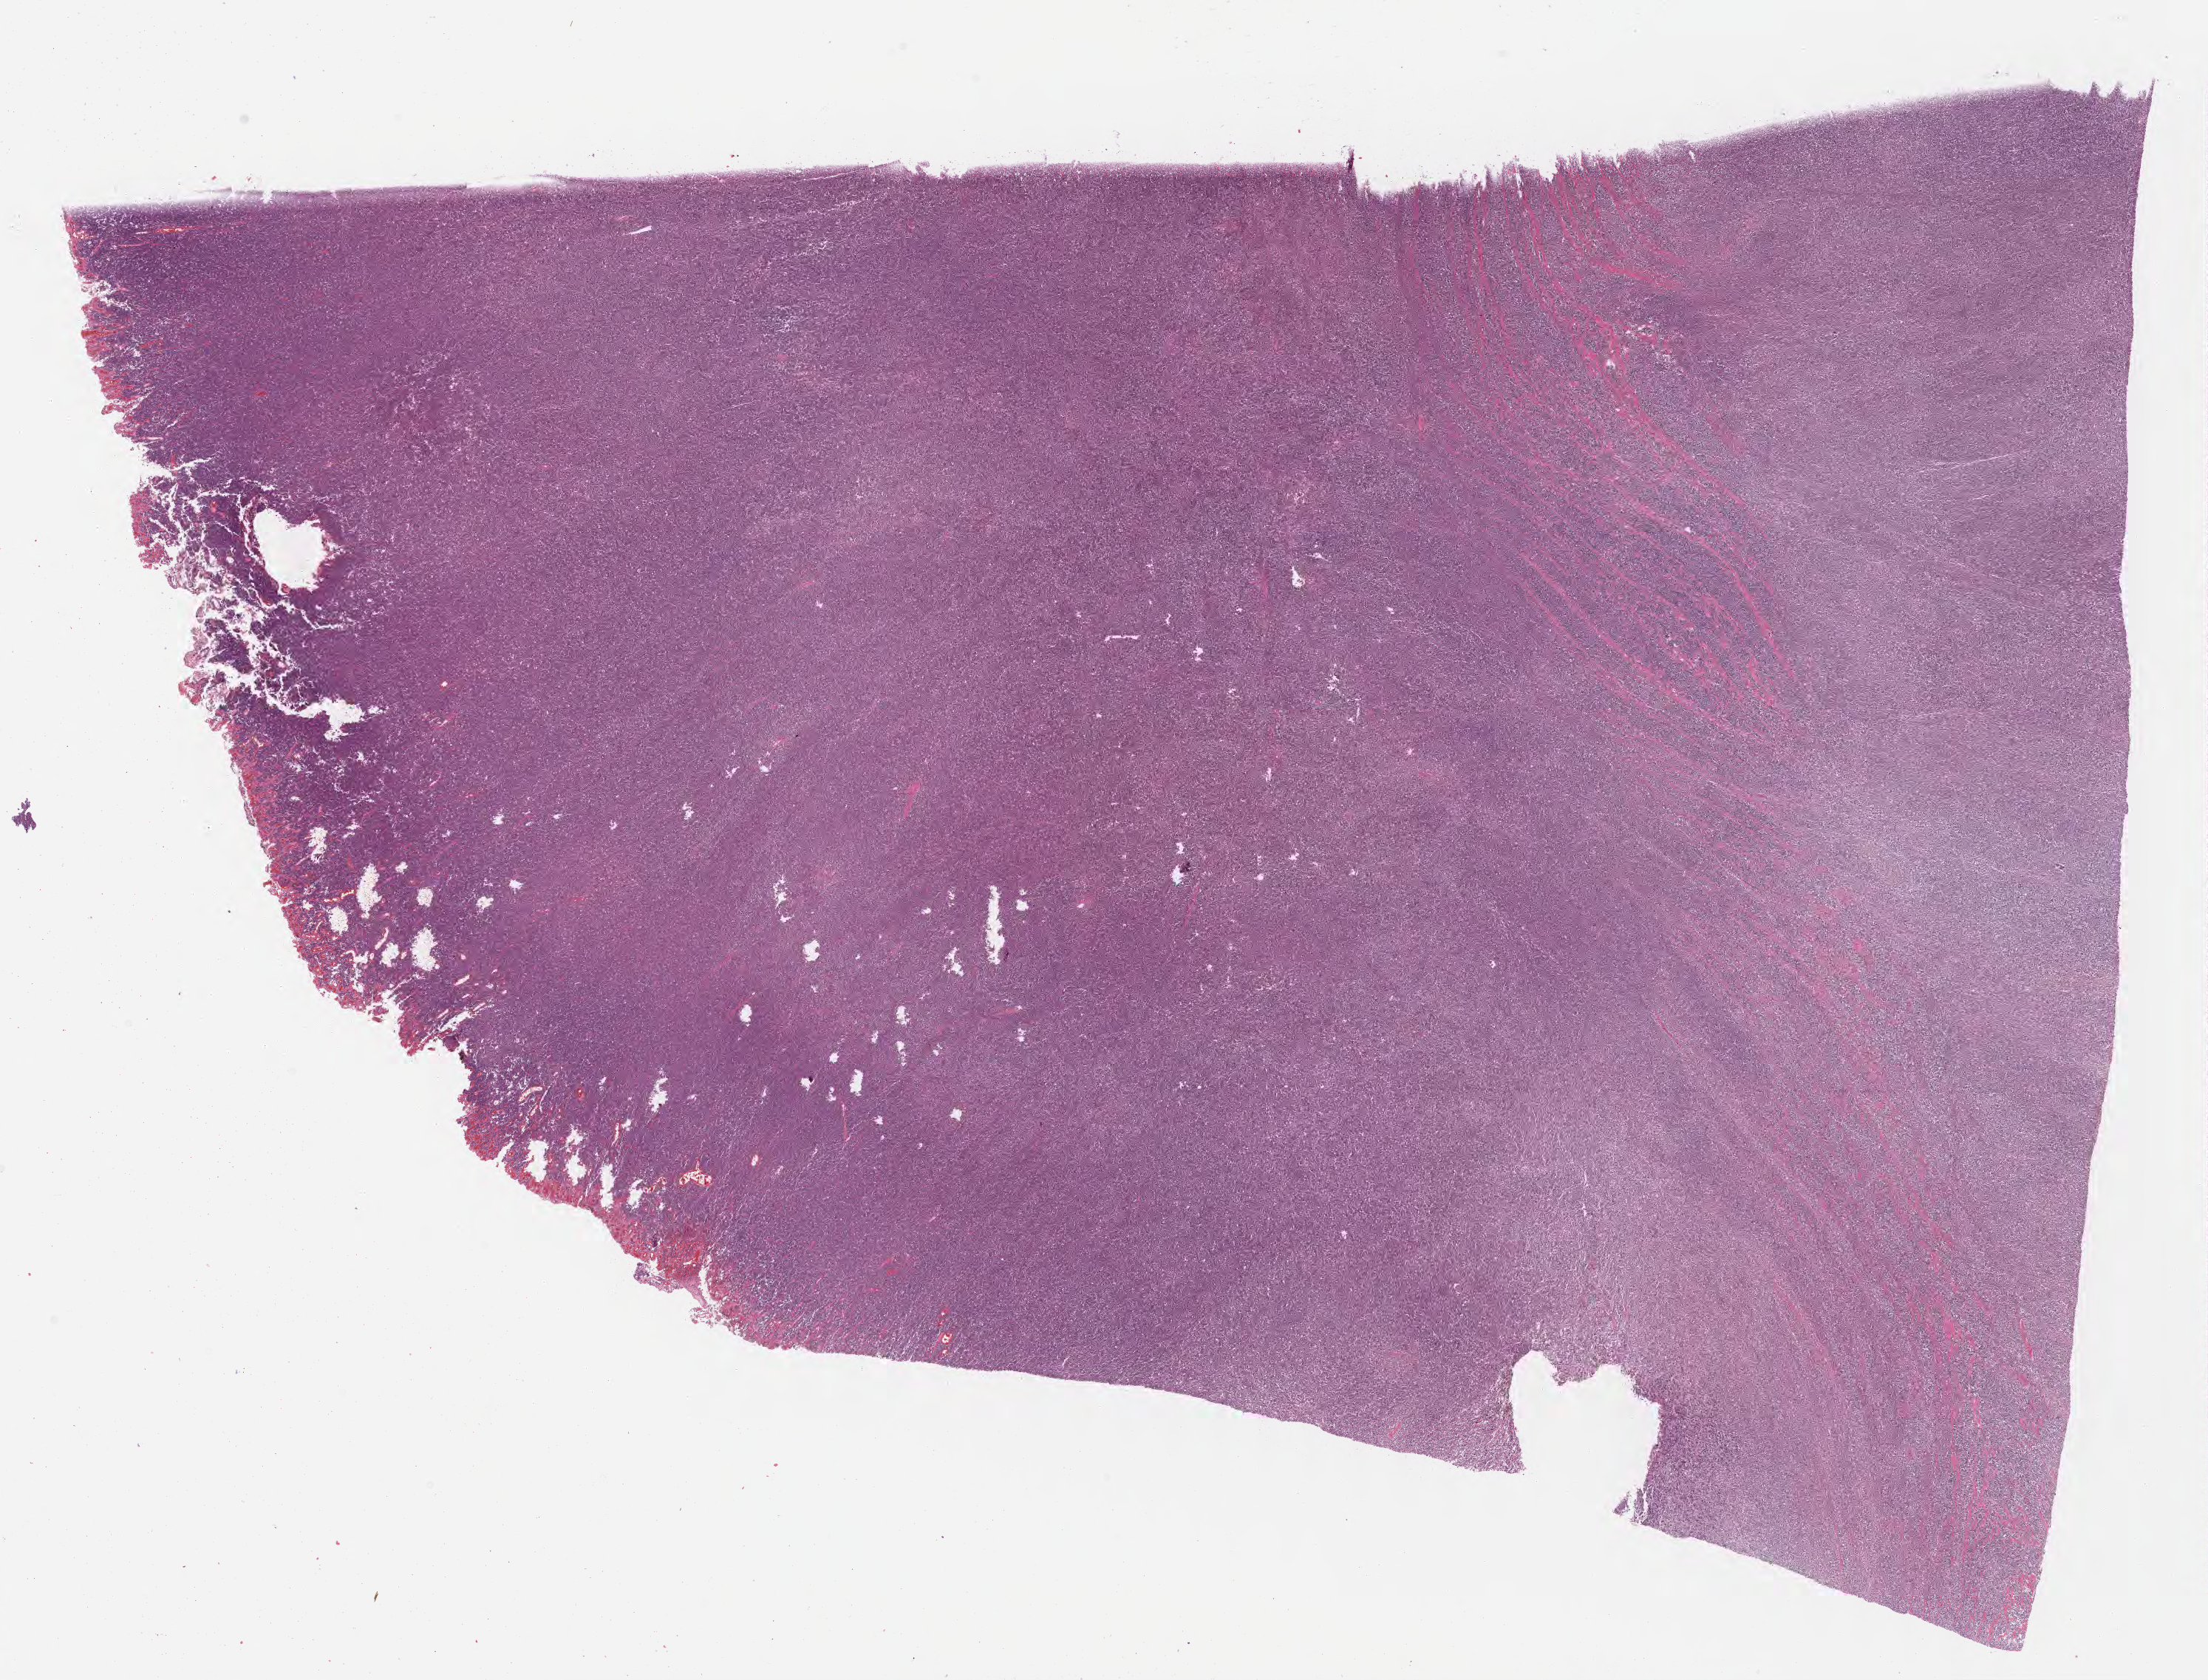
Digitized hematoxylin and eosin (H&E)-stained section, low-resolution overview of the scanned area, about 24.1 x 18.4 mm. Tumor tissue. Patient male; aged 17.
• histologic diagnosis: Burkitt lymphoma, NOS